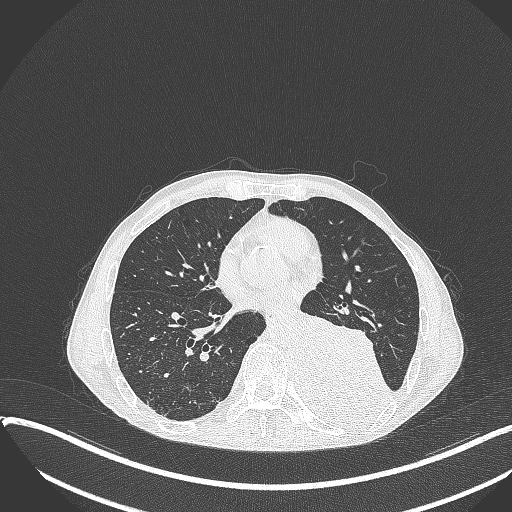
Chest CT, one axial slice. Position 156 of 401 along the scan axis. Lung window (W 1500 / L -600 HU). 512 × 512 image matrix, field of view 400 × 400 mm. Male patient, age 57 years. Case-level facts recorded for this patient, not image findings: clinical TNM (as recorded): T4 N0 M0.
Outlined on this slice (rectangle marked by the reading radiologist):
- lung tumour (recorded histology: squamous cell carcinoma): bounding box [x1, y1, x2, y2] px = [292, 307, 391, 424]